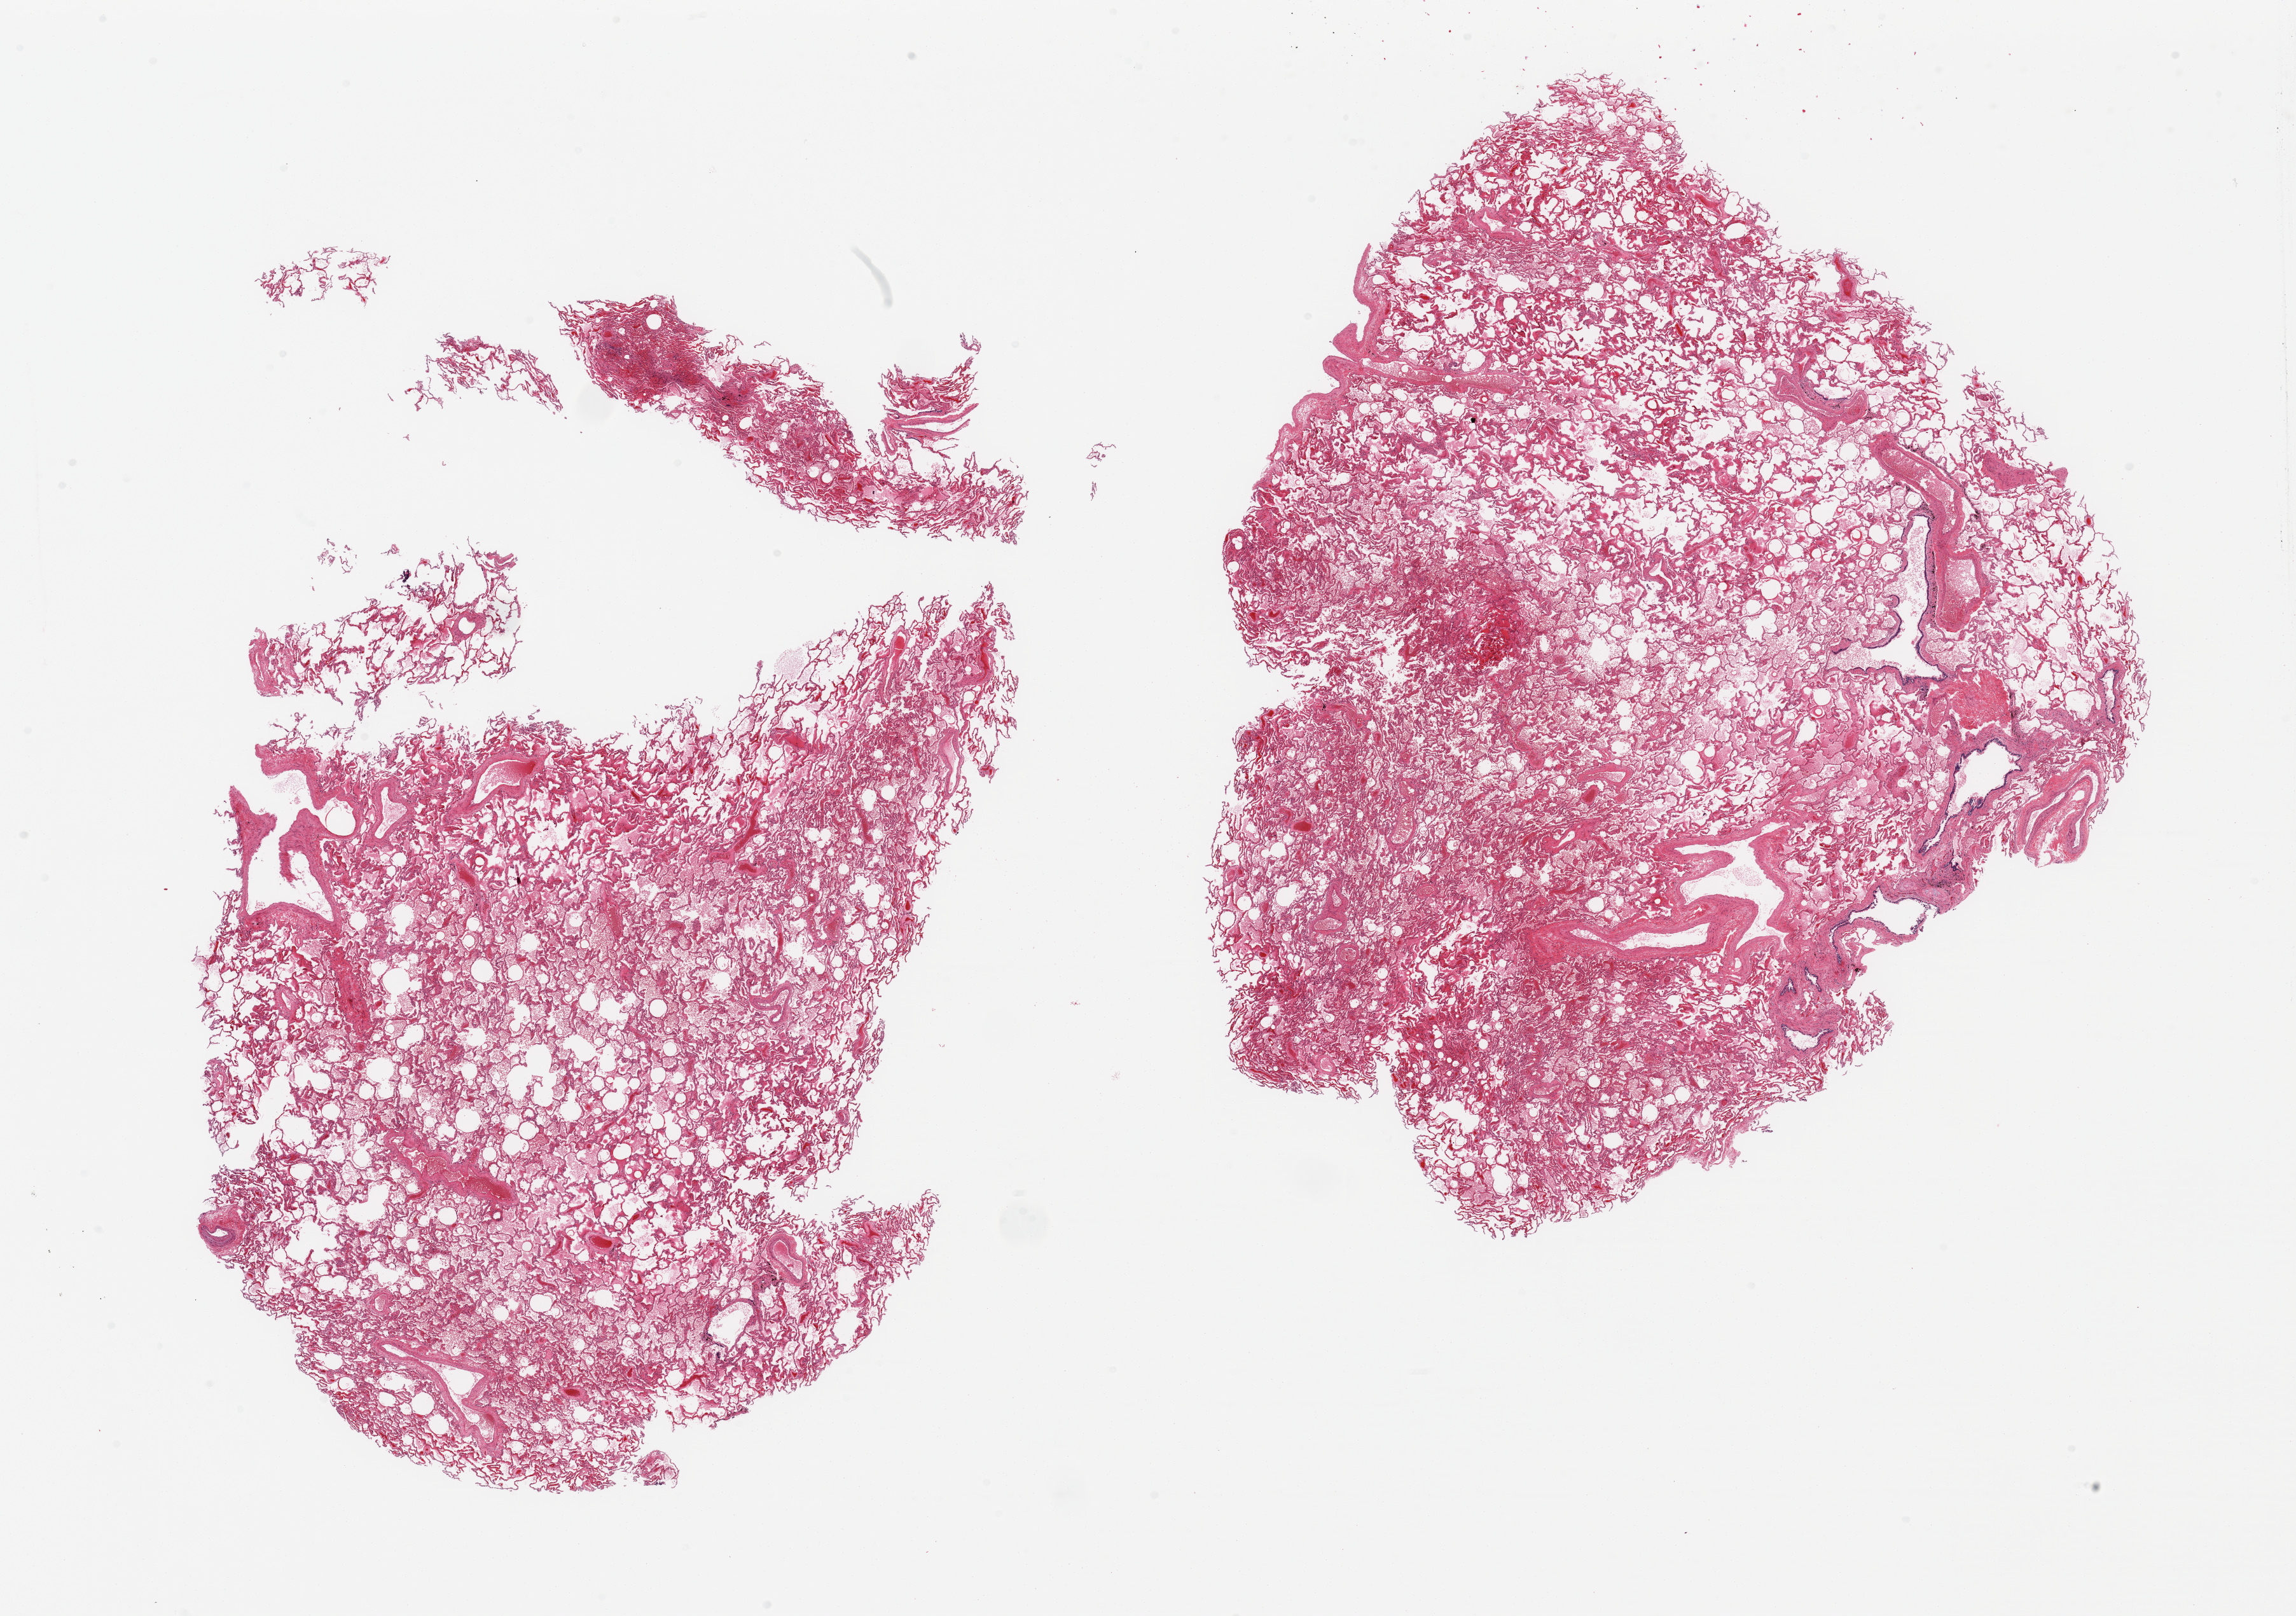
Digitized hematoxylin and eosin (H&E)-stained section, brightfield — a low-resolution overview of the entire scanned area, about 28.5 x 20.1 mm (acquisition: 20x scan), PAXgene-fixed, paraffin-embedded tissue, section of lung (target tissue), tissue donor sample.
Pathologist's review note for this sample: 2 pieces, moderate congestion.